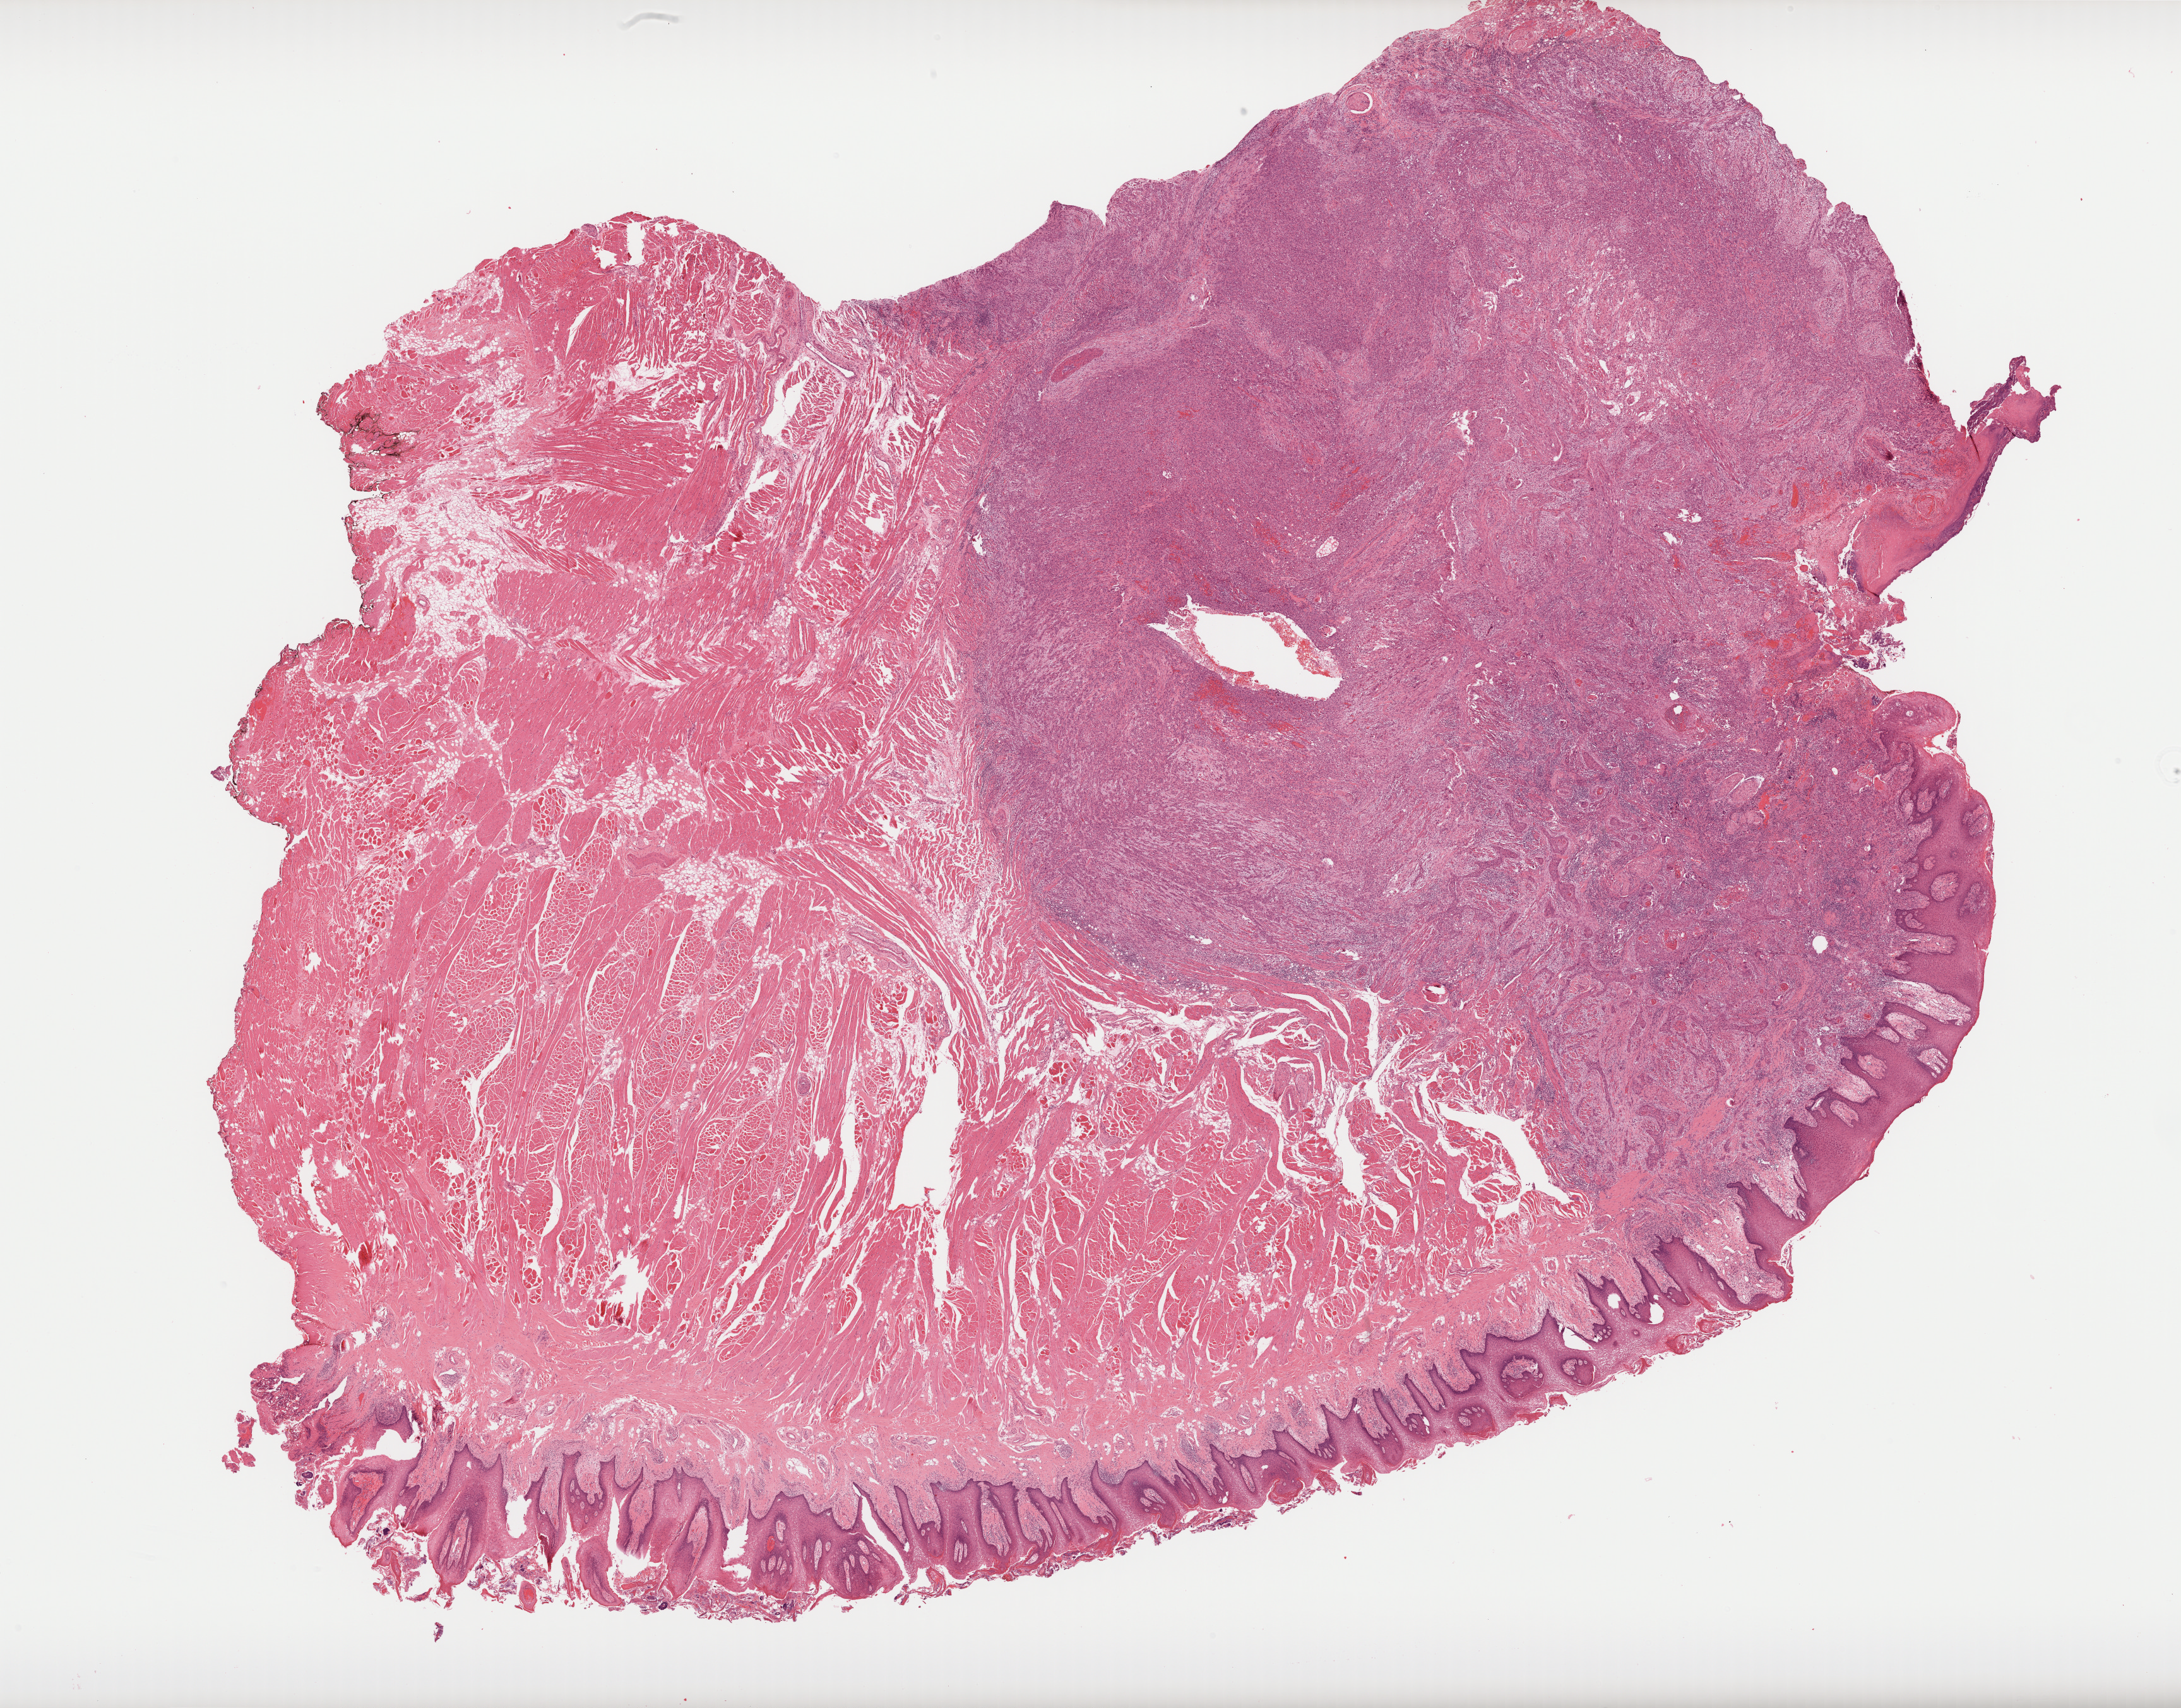
Digitized H&E-stained tissue section (whole slide), low-resolution overview of the scanned area, about 27.8 x 21.8 mm. Formalin-fixed paraffin-embedded (FFPE) diagnostic section. Primary tumour sample from the head and neck. Male, age 52 years at initial diagnosis. Histologic grade: G3 (poorly differentiated).
Histologic diagnosis: Squamous cell carcinoma, NOS (tongue, NOS). TNM: T2 N2b. AJCC pathologic stage: IVA (6th edition).